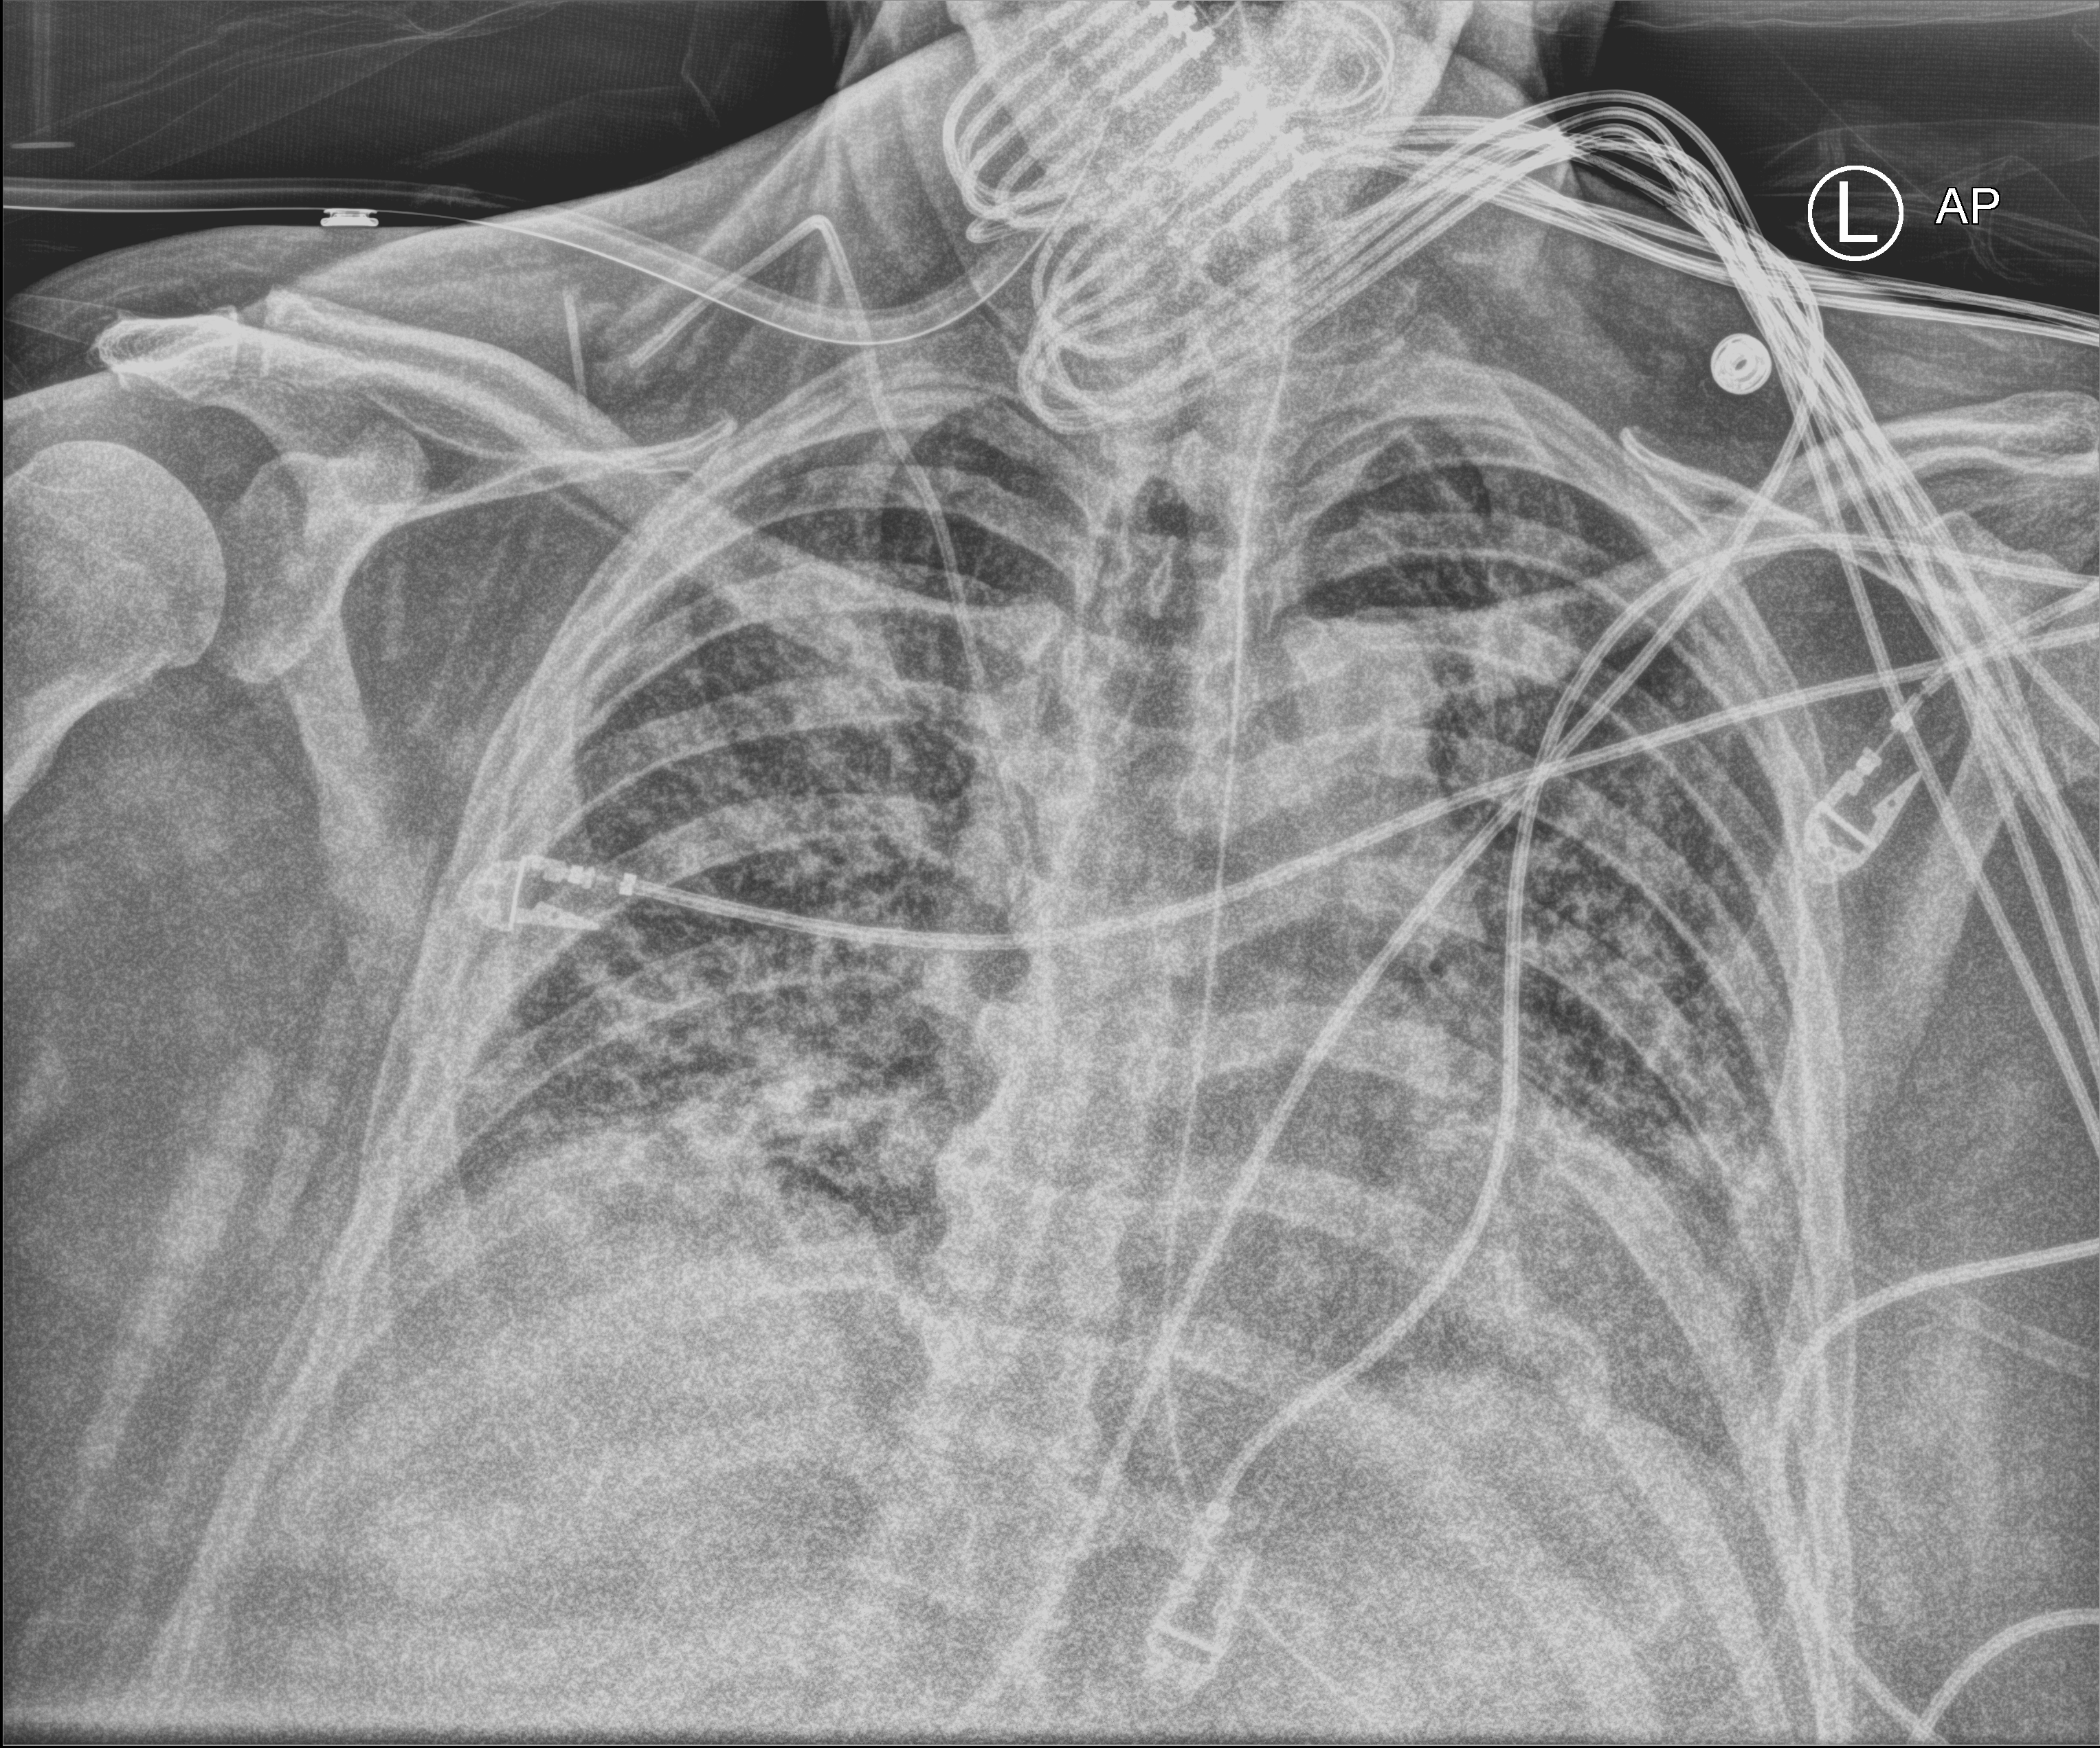
Portable chest radiograph, anteroposterior (AP) projection. Patient hospitalised with COVID-19; male, aged 60–74 years.
From the hospital-stay record, not from the radiograph (when in the stay this image was taken is not recorded):
- length of hospital stay: 40 days